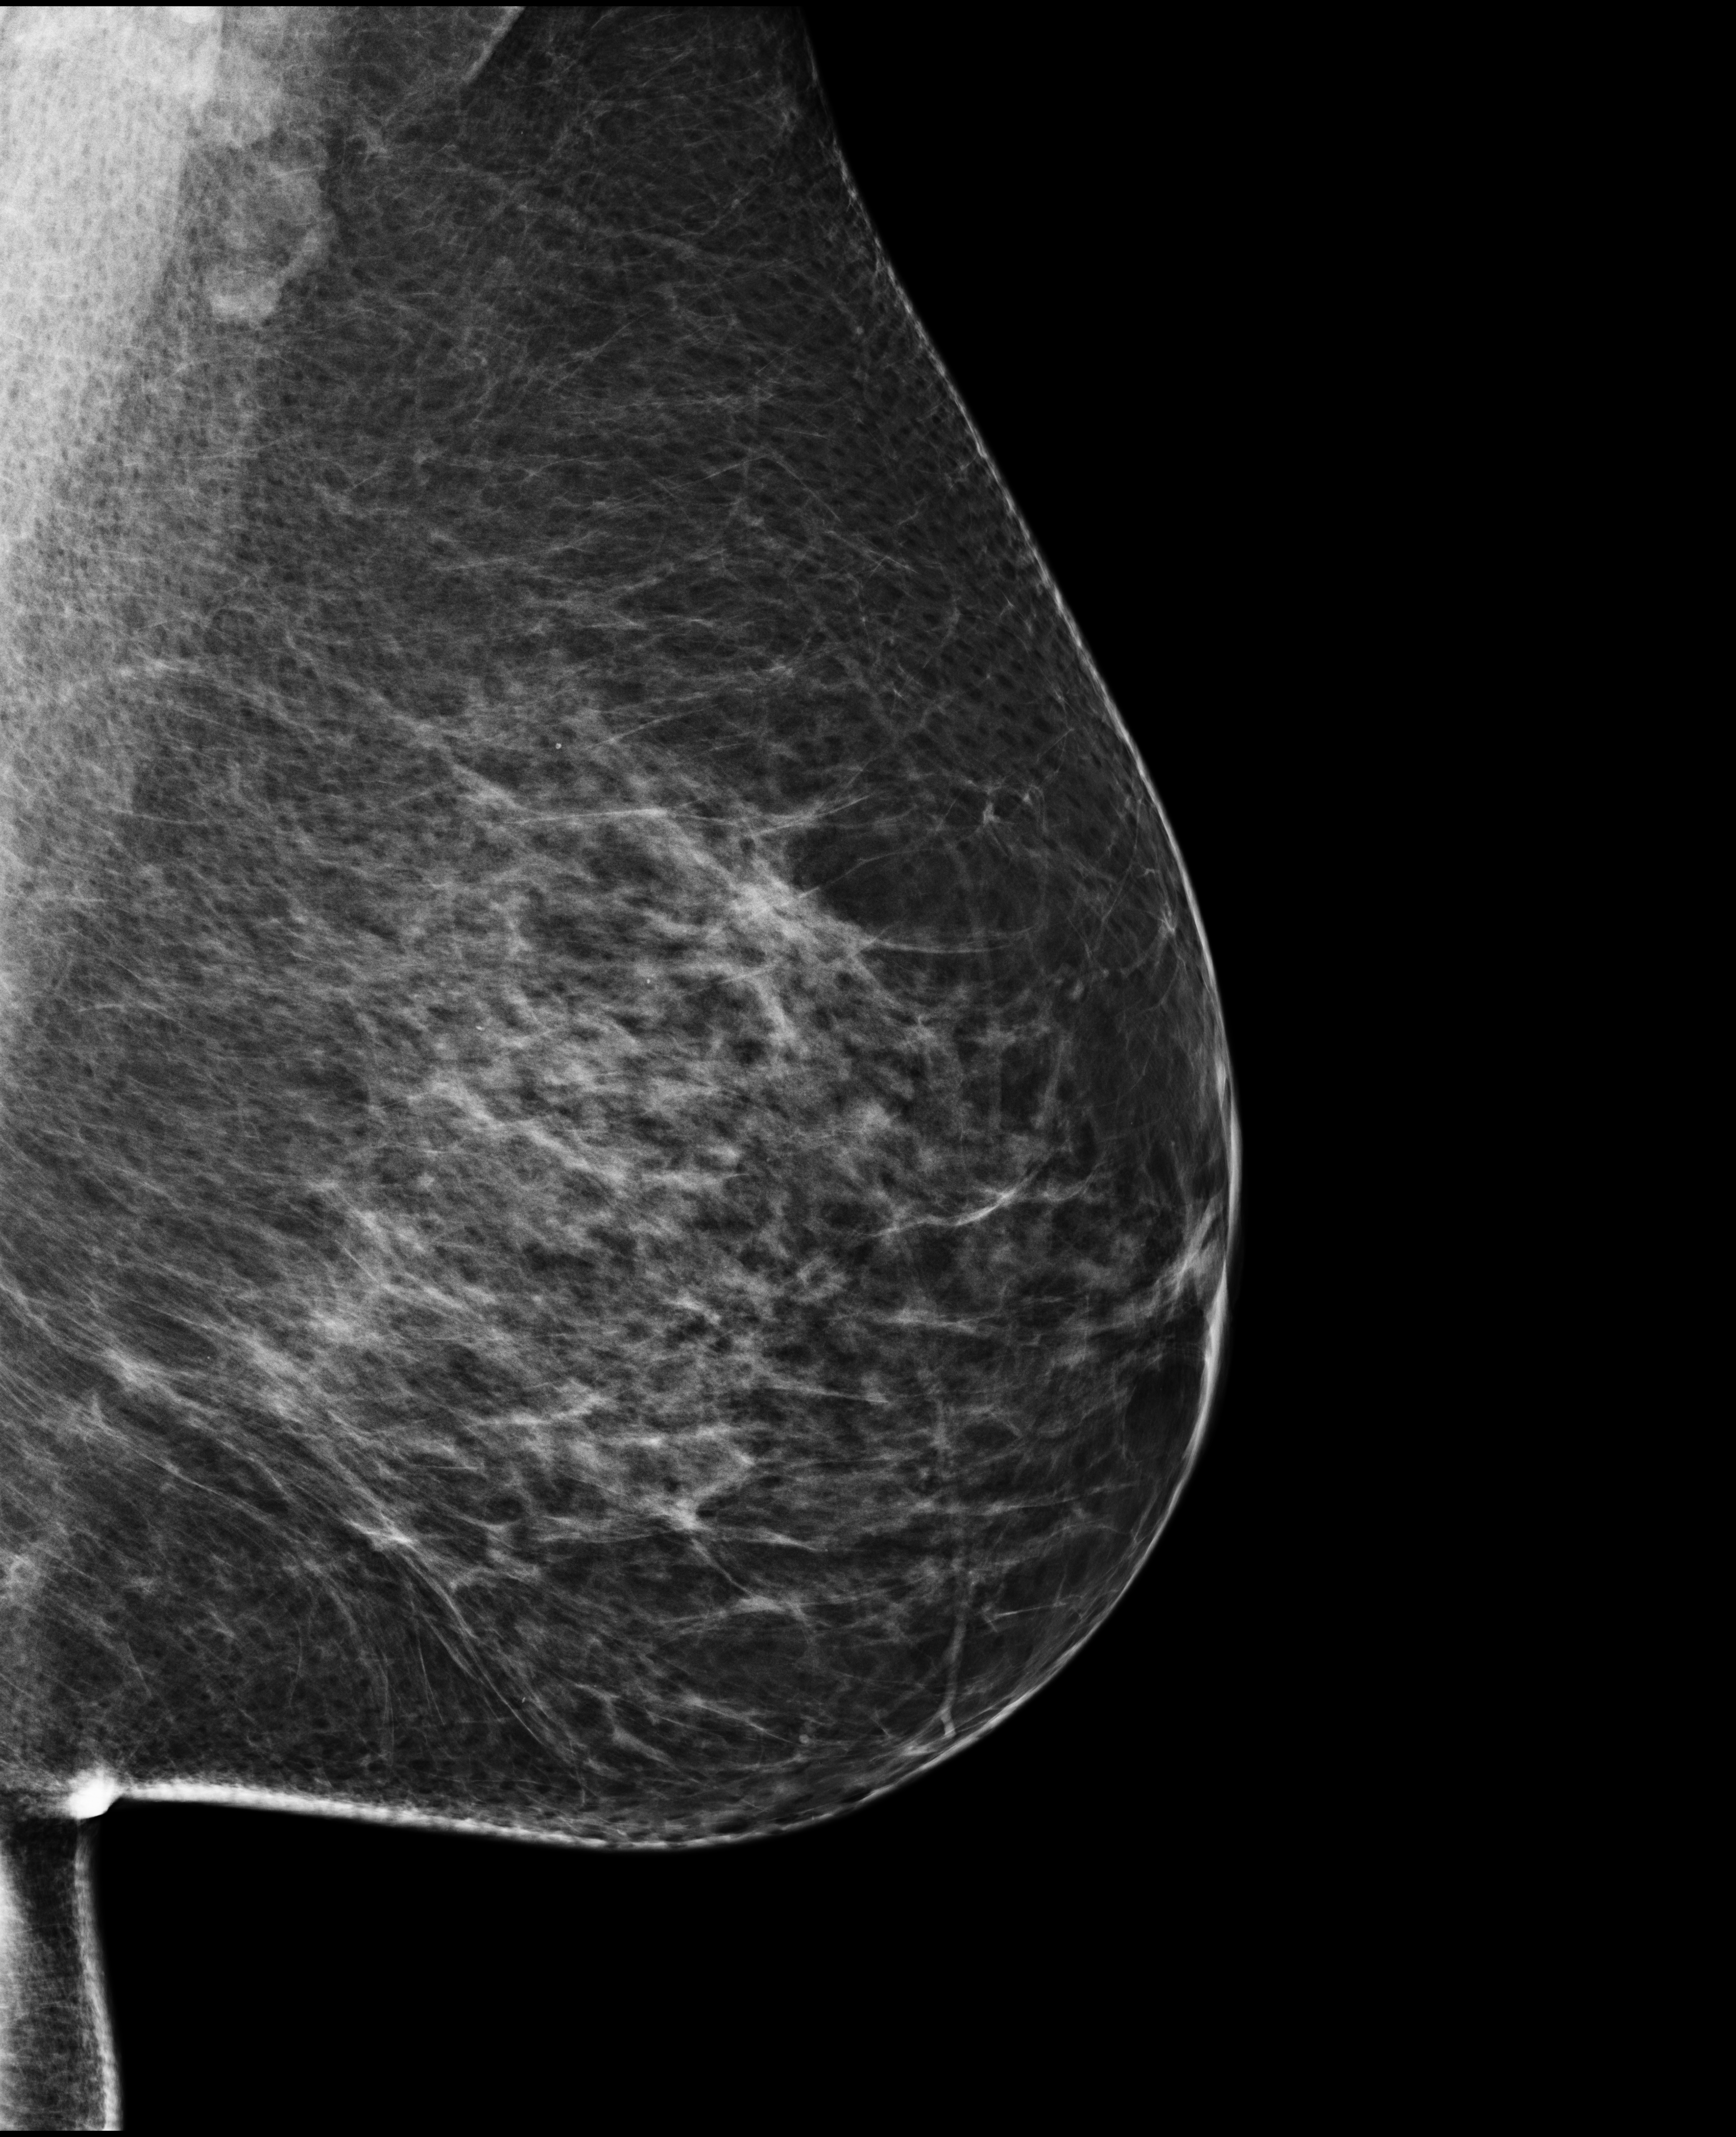
Diagnostic examination (additional views); system: Selenia Dimensions. Patient: female, 56 years.
Image type: full-field digital mammogram. Breast: left. Projection: medio-lateral oblique projection. BI-RADS breast density category at the screening exam (both breasts, scale 1–4): 3. Final BI-RADS category for the screening round (tomosynthesis exam, both breasts): category 5. Recall: recalled for additional imaging after this screen.